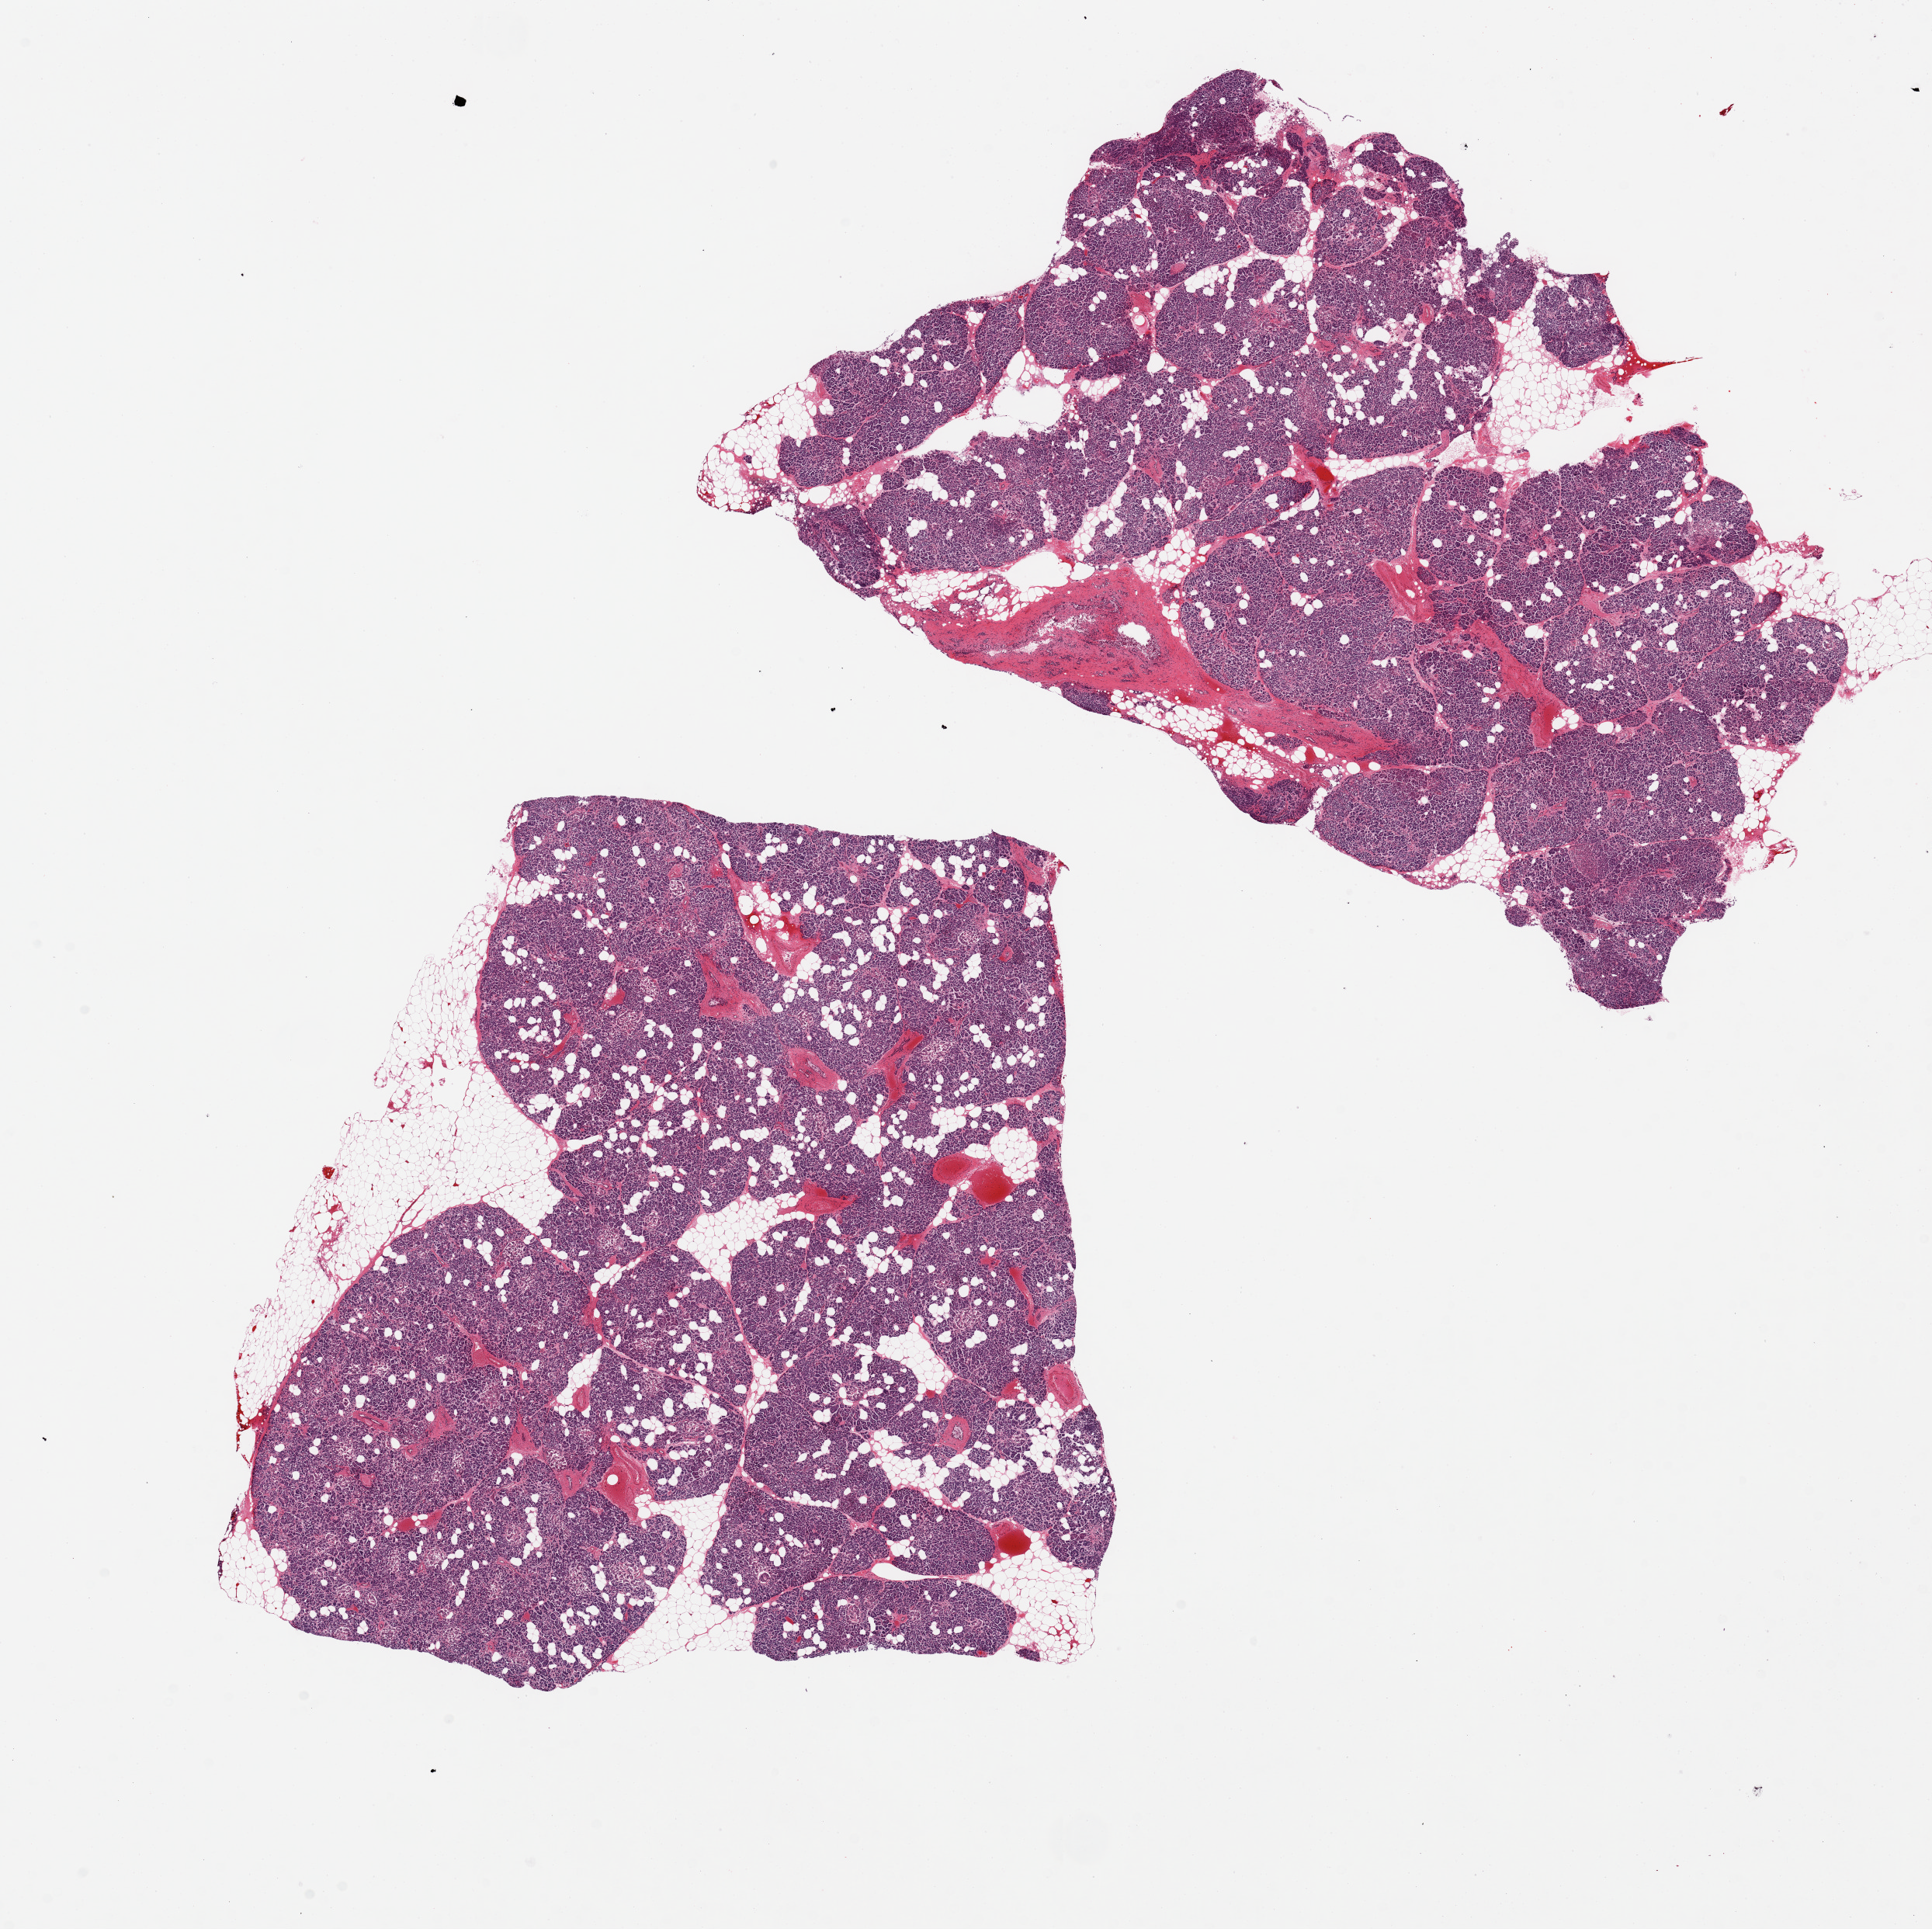
Digitized haematoxylin and eosin-stained section, low-resolution overview of the scanned area, about 19.7 x 19.7 mm (slide scanned at 20x). PAXgene-fixed, paraffin-embedded tissue. Sampled site (target tissue): pancreas. Donor tissue sample. Donor: male.
Reviewer comment on this tissue sample: 2 pieces. 20% internal fat and 10% external fat.